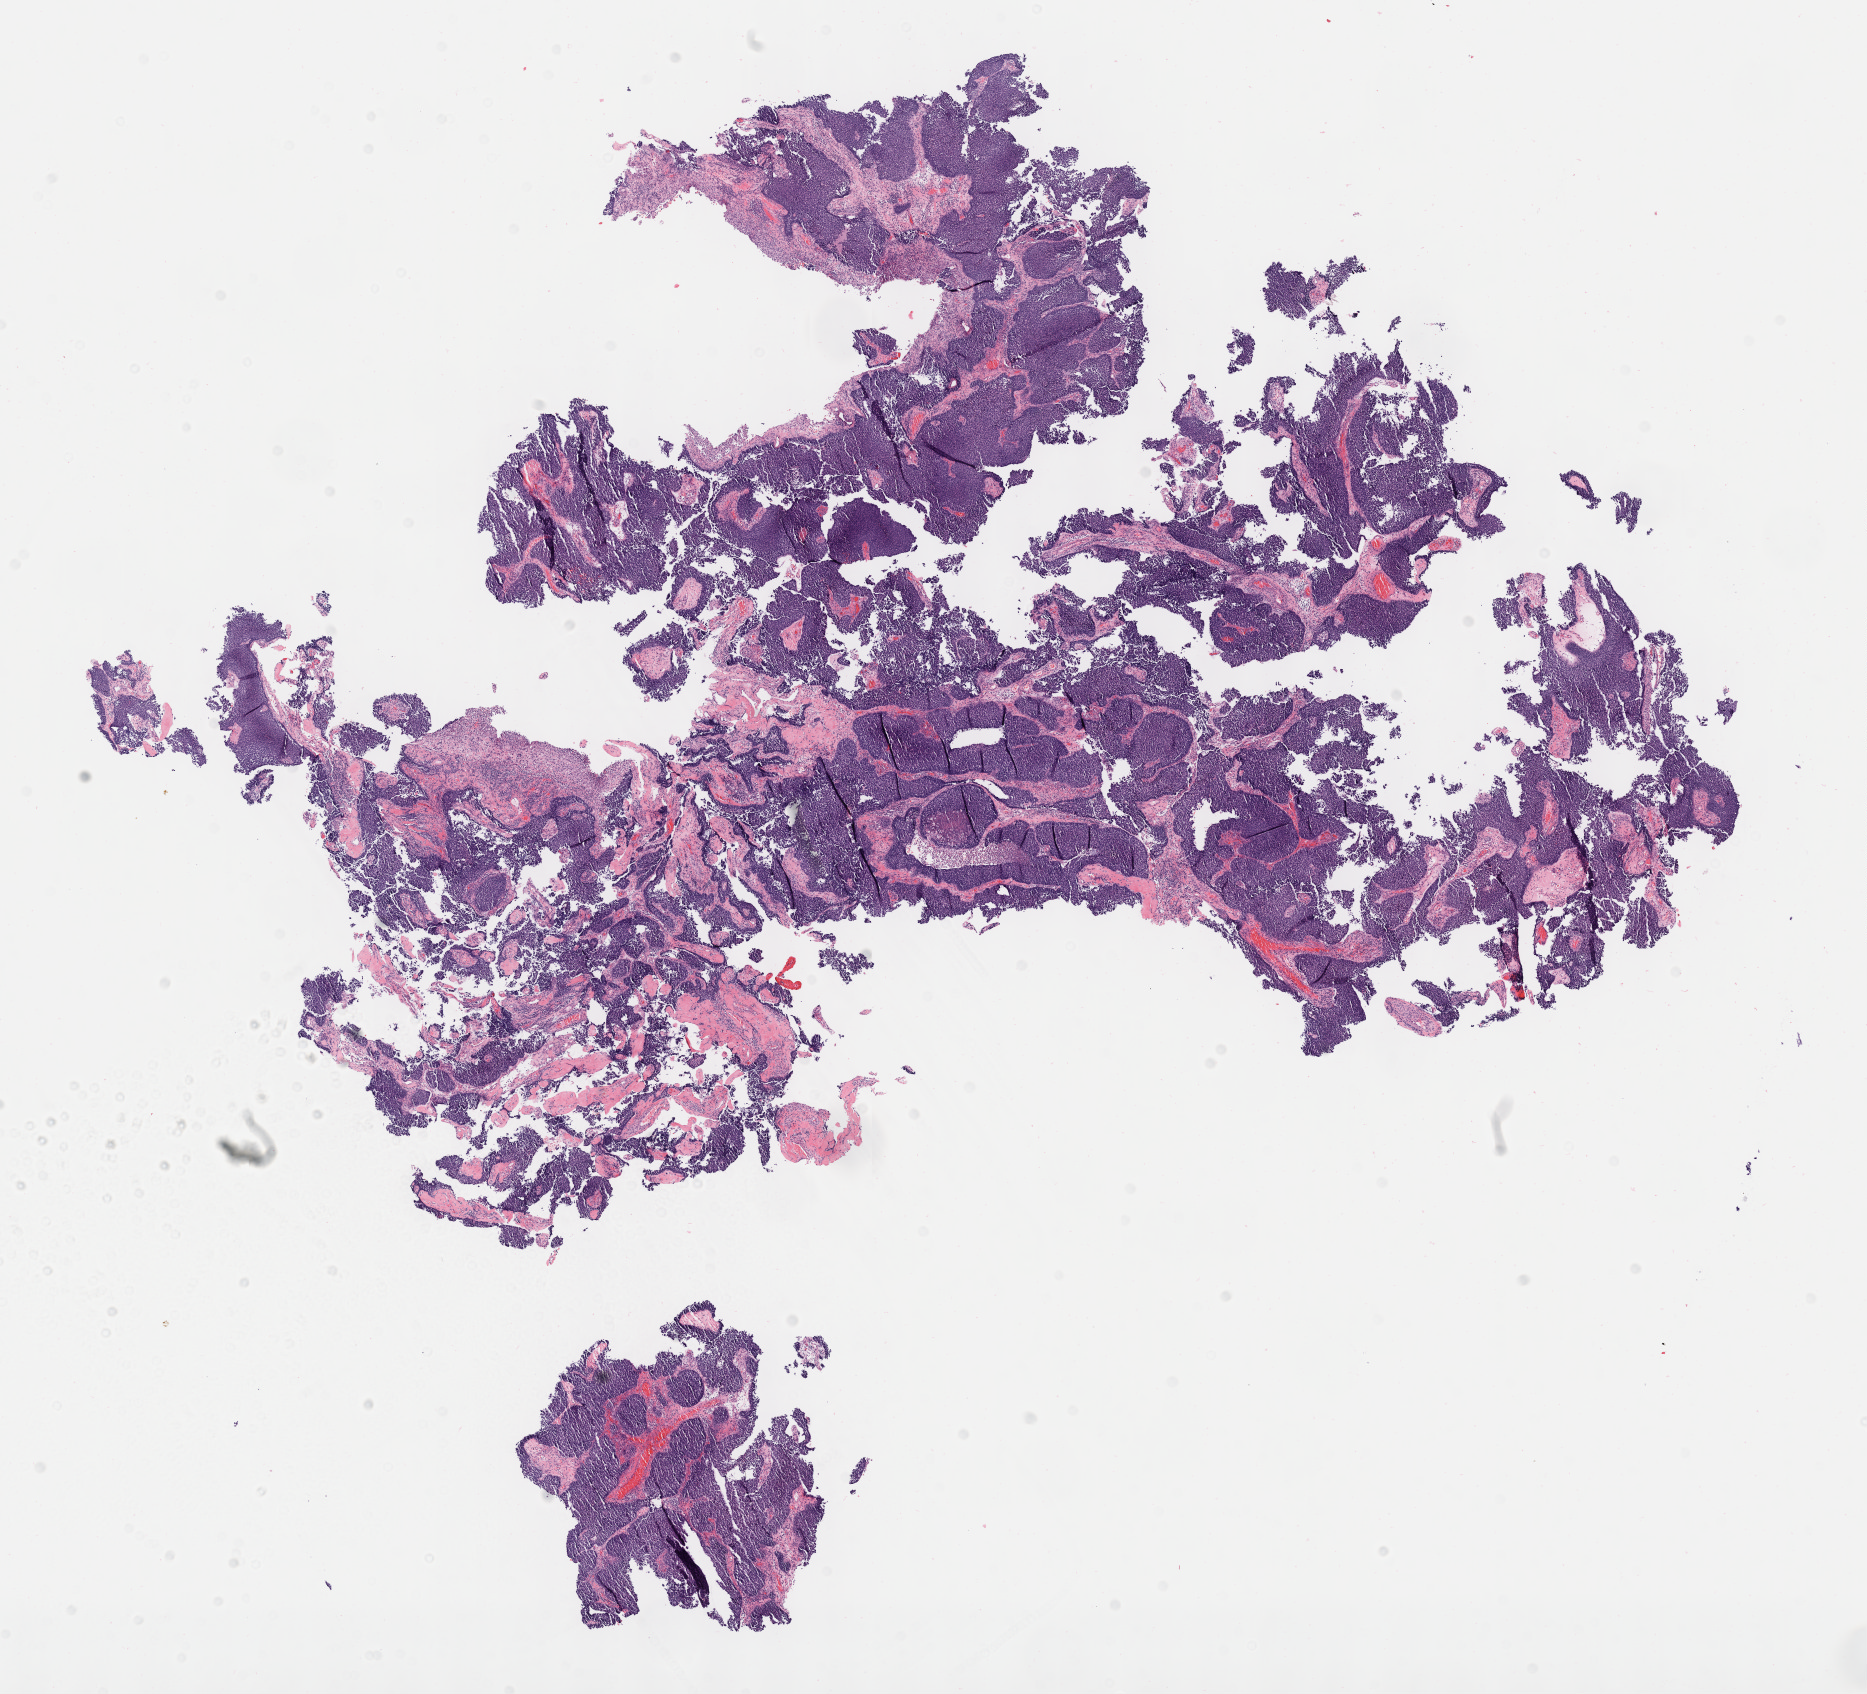
Digitized H&E-stained section — low-resolution overview of the scanned area, about 15.1 x 13.7 mm, tumor tissue, site: cervix. Female patient, aged 80.
Histologic diagnosis: Carcinoma, NOS.